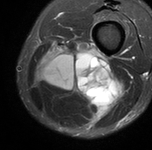
MRI of an extremity soft-tissue mass, one axial slice. Slice 30 of 90 in the series (ordered by position). STIR. MR volume resampled by the dataset authors to the PET/CT grid (not the native acquisition matrix). 3.27 mm slice thickness. 152 × 150 image matrix. Male patient. Case-level facts recorded for this patient, not image findings: histological type: undifferentiated pleomorphic liposarcoma; grade: high; site of the primary tumour: left thigh.
Annotated regions visible in this slice (expert contour drawn on MRI and transferred to this co-registered scan by the dataset authors):
- gross tumour volume including surrounding oedema: box from (x=36, y=41) to (x=120, y=122) px
- gross tumour volume (mass): (x=48, y=60)–(x=110, y=102)